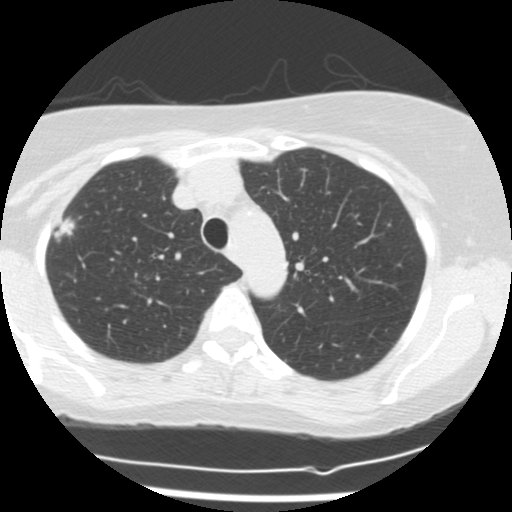
Low-dose screening chest CT, one axial slice; position 120 of 160 along the scan axis; reconstruction kernel STANDARD; 120 kVp; lung window (W 1500 / L -600 HU); 512 × 512 image matrix, field of view 300 × 300 mm.
Structures marked on this image (outlined manually by an expert reader):
- lesion 1 (tumor, upper lobe of right lung): bounding box (x1, y1, x2, y2) in pixels: (53, 217, 75, 242)